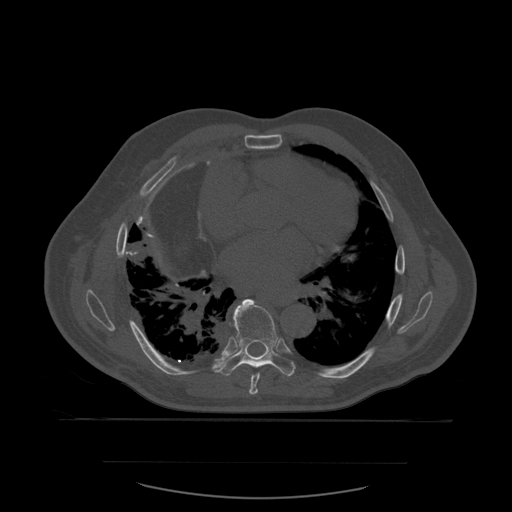
CT including the spine, one axial slice. Bone window (W 1800 / L 400 HU). 1.25 mm slice thickness. 512 × 512 image matrix, field of view 479 × 479 mm. Patient age 71 years. From the clinical record (not read from this slice): primary cancer: lung.
Annotated regions visible in this slice (semi-automatically segmented with operator editing):
- T7 vertebra: bounding box <249,373,260,395> (left, top, right, bottom; pixels)
- T8 vertebra: <219,299,296,377>